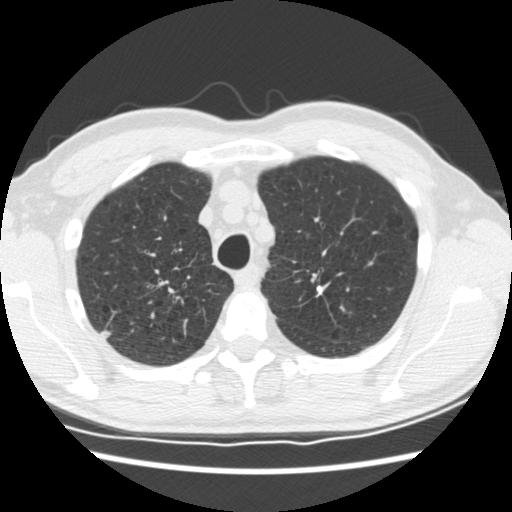
Low-dose screening chest CT, one axial slice; slice 143 of 183 in the series (ordered by position); 120 kVp; lung window (W 1500 / L -600 HU); 512 × 512 image matrix, field of view 339 × 339 mm.
Structures marked on this image (manually delineated by an expert):
- lesion 2 (tumor, upper lobe of right lung): box from (x=100, y=330) to (x=112, y=339) px